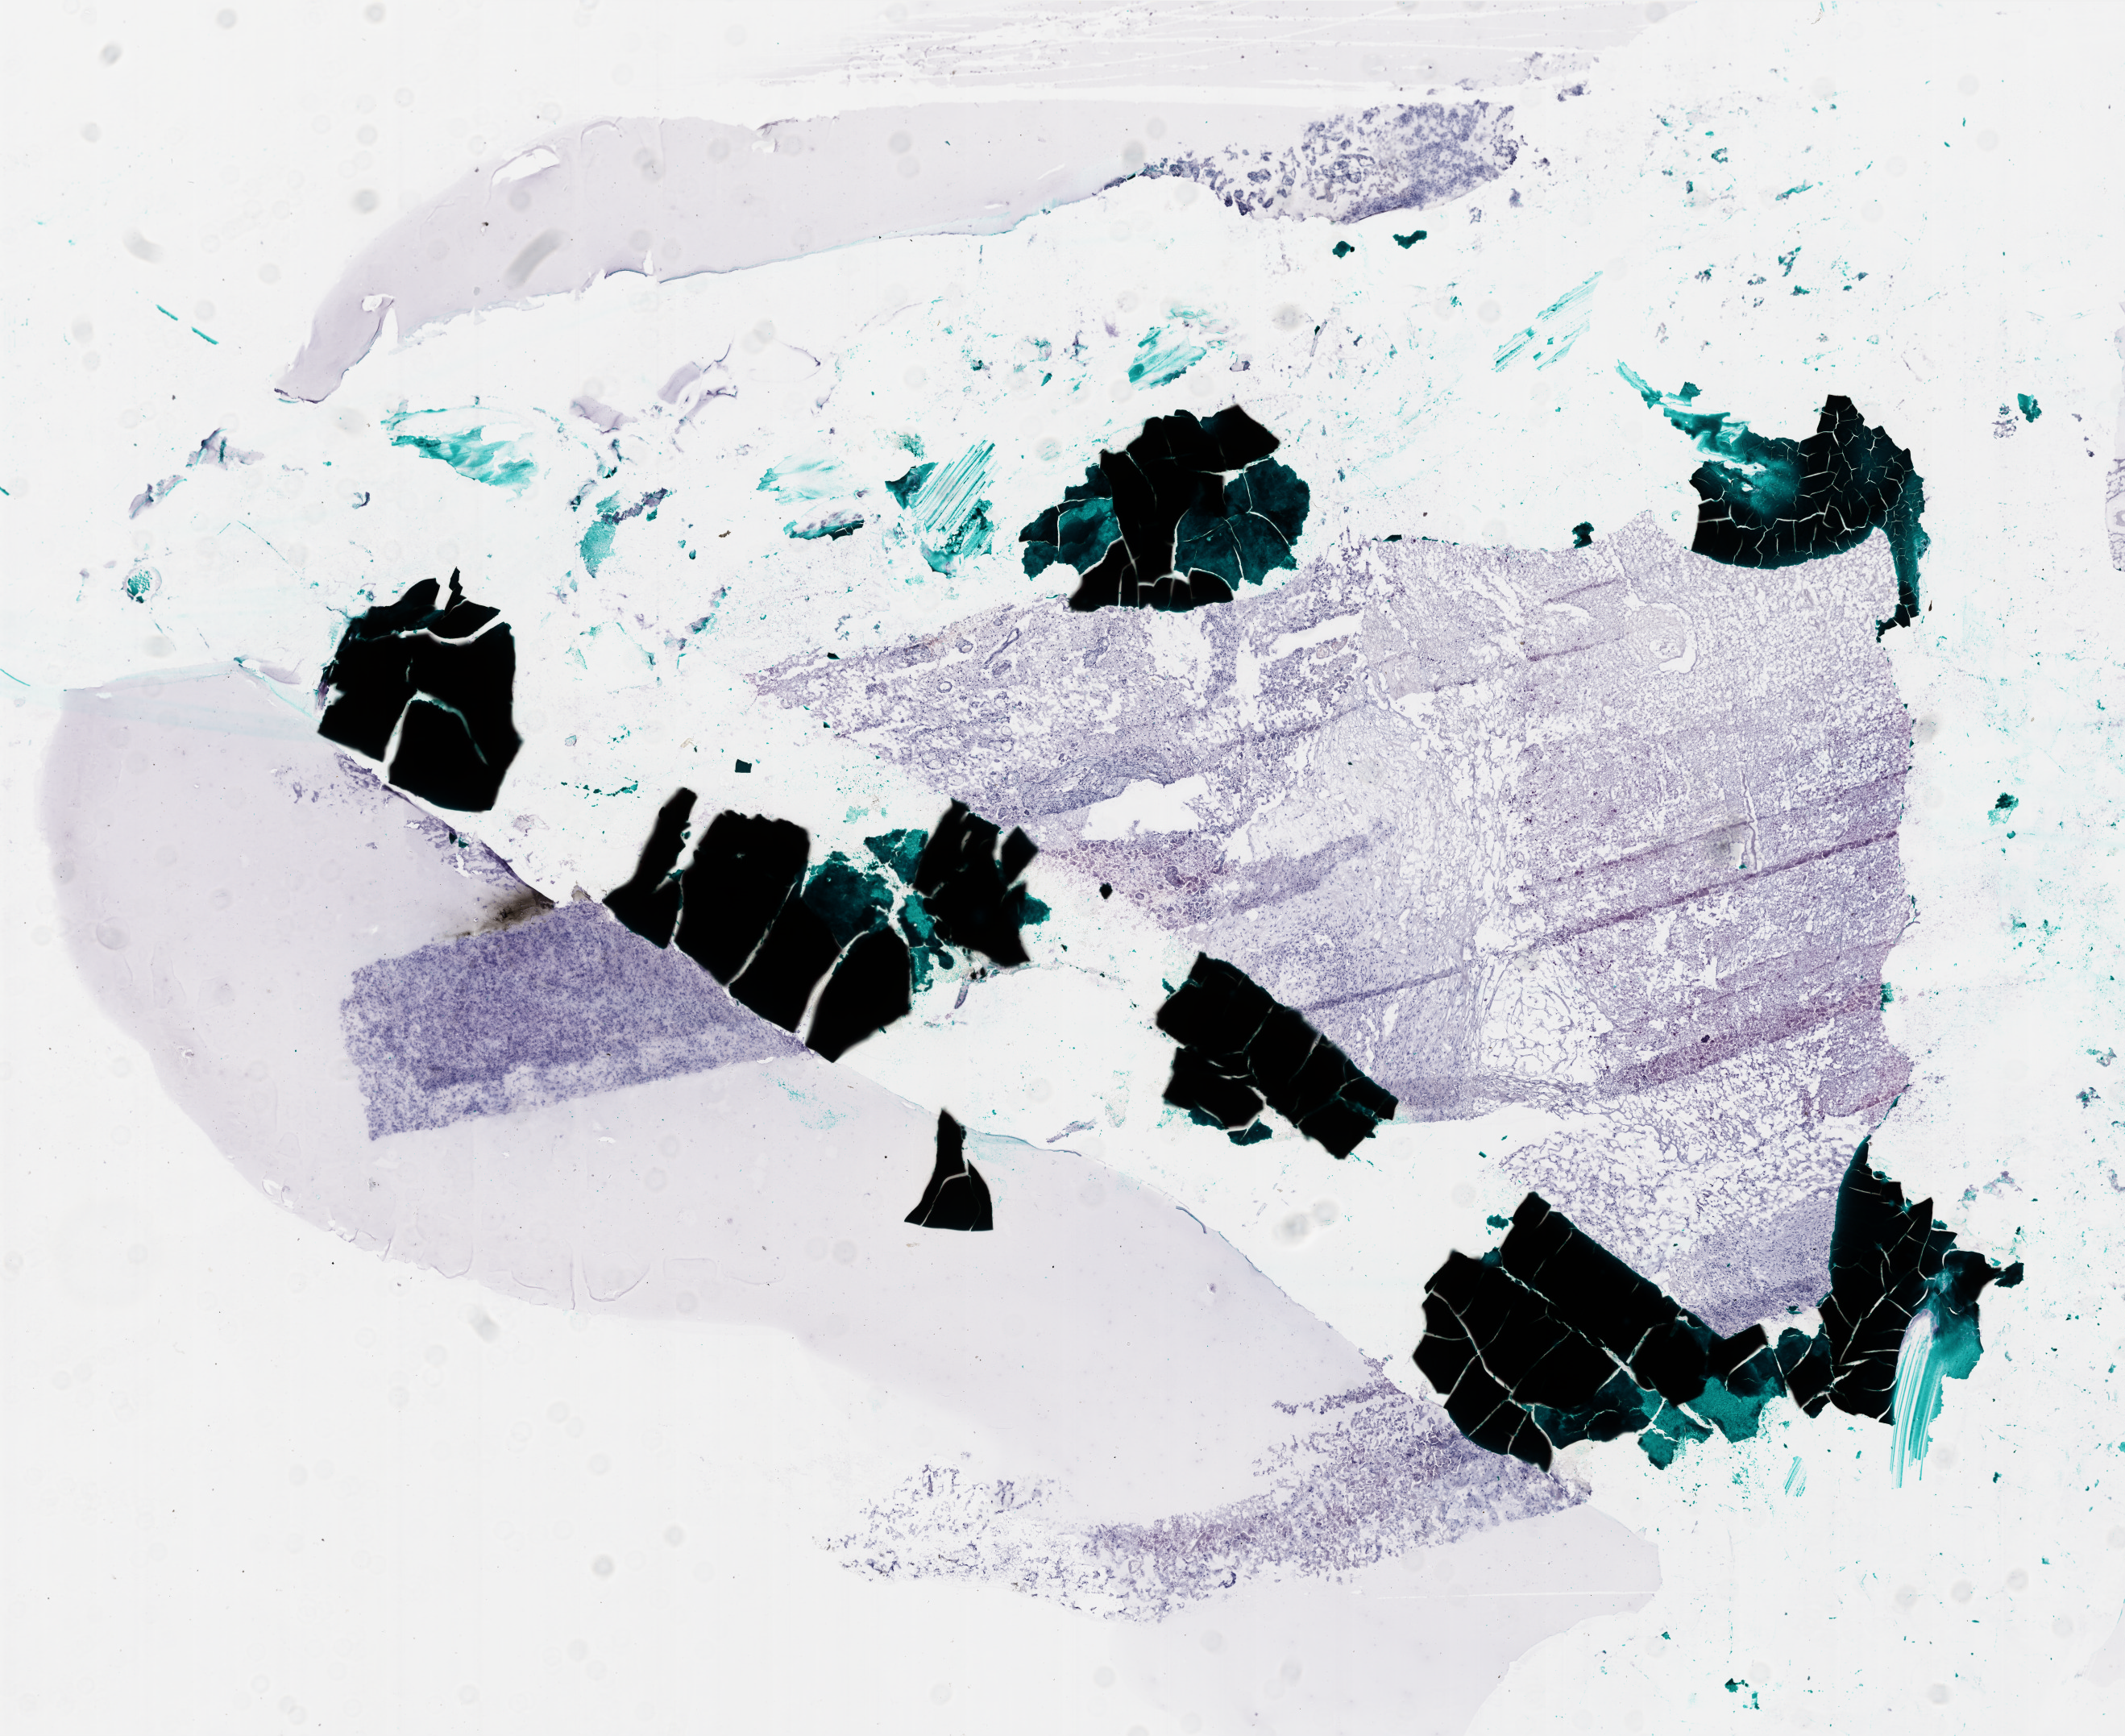
Whole-slide histology image, H&E — shown as a low-resolution overview of the whole scanned area (about 10.6 x 8.7 mm, slide scanned at 20x); frozen section from the bottom of the tissue portion; primary tumour sample from the brain. Female patient; age at initial diagnosis 63 years. Composition of this section per pathologist review: tumour cells 10%, tumour nuclei 100%, normal cells 0%, stromal cells 0%, necrosis 90%. Inflammatory infiltration, as recorded: lymphocyte infiltration 0%, monocyte infiltration 0%, neutrophil infiltration 0%.
- histologic diagnosis: Glioblastoma